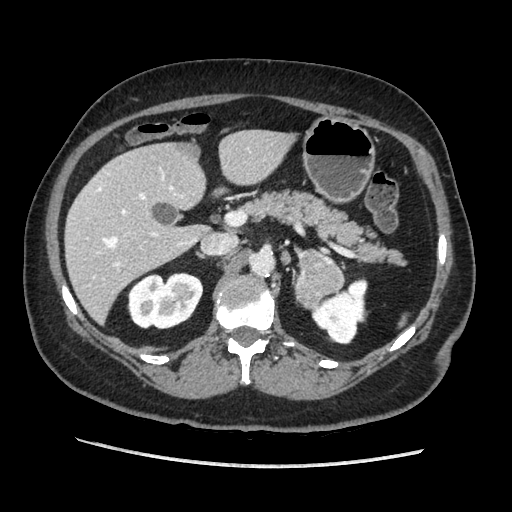
Contrast-enhanced abdominal CT, one axial slice; slice 115 of 203 in the series (ordered by position); soft-tissue window (W 400 / L 40 HU); 1.25 mm slice thickness; 512 × 512 image matrix. Female patient. From the clinical record (not read from this slice): diagnosis: adrenocortical carcinoma; tumour side: left adrenal.
Outlined on this slice (semi-automatic segmentation, software-assisted and operator-edited):
- mass: bounding box [x1, y1, x2, y2] px = [298, 250, 344, 304]